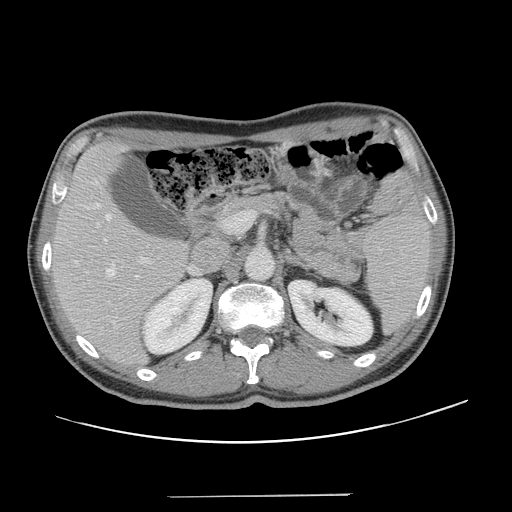
Contrast-enhanced abdominal CT, one axial slice; position 79 of 131 along the scan axis; intravenous contrast given; soft-tissue window (W 400 / L 40 HU); 512 × 512 image matrix, field of view 403 × 403 mm. Male patient, age 60 years. From the clinical record (not read from this slice): diagnosis: colorectal cancer liver metastases, imaged before liver resection; multiple liver metastases: no; largest metastasis: 2.5 cm; disease in both lobes: no.
Outlined on this slice (expert manual segmentation):
- hepatic veins: box from (x=97, y=204) to (x=138, y=277) px
- liver: (x=53, y=143)–(x=187, y=365)
- planned liver remnant (the part of the liver to remain after resection): (x=53, y=143)–(x=187, y=359)